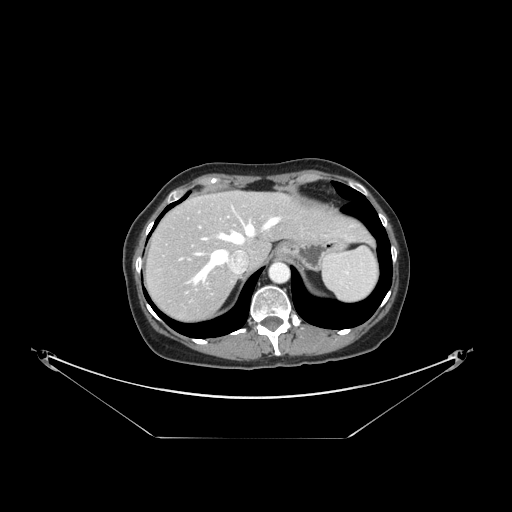
Contrast-enhanced abdominal CT, one axial slice. Position 120 of 148 along the scan axis. 120 kVp. Intravenous contrast given. Soft-tissue window (W 400 / L 40 HU). 2.5 mm slice thickness. 512 × 512 image matrix, field of view 500 × 500 mm. Female patient, age 73 years. Case-level facts recorded for this patient, not image findings: diagnosis: colorectal cancer liver metastases, imaged before liver resection; multiple liver metastases: no; largest metastasis: 1 cm; disease in both lobes: no.
Structures marked on this image (manually delineated by an expert):
- hepatic veins: bounding box <192,207,281,284> (left, top, right, bottom; pixels)
- liver: <147,193,369,319>
- planned liver remnant (the part of the liver to remain after resection): <173,192,368,265>